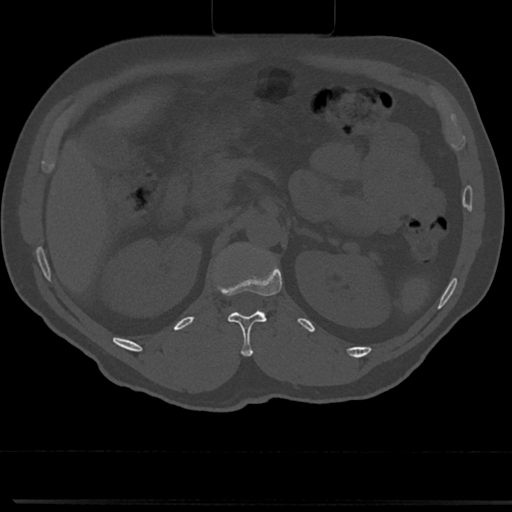
CT including the spine, one axial slice; slice 125 of 817 in the series (ordered by position); 120 kVp; bone window (W 1800 / L 400 HU); 0.5 mm slice thickness; 512 × 512 image matrix, field of view 355 × 355 mm. Male patient, age 61 years. Case-level facts recorded for this patient, not image findings: primary cancer: prostate.
Outlined on this slice (semi-automatic segmentation, software-assisted and operator-edited):
- L1 vertebra: bounding box (x1, y1, x2, y2) in pixels: (212, 241, 273, 319)
- T12 vertebra: (226, 281, 281, 356)